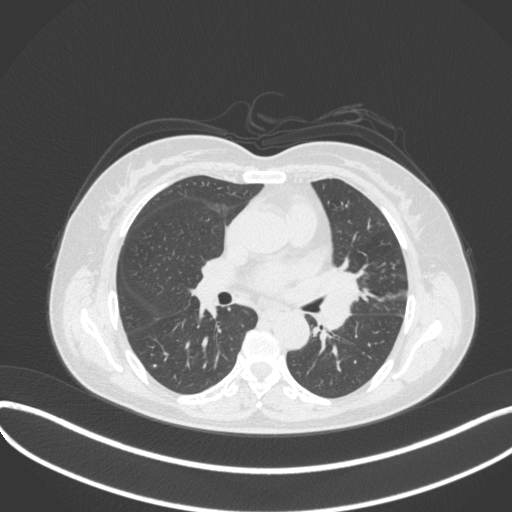
Chest CT, one axial slice; slice 191 of 373 in the series (ordered by position); reconstruction kernel B31f; 120 kVp; lung window (W 1500 / L -600 HU); 1 mm slice thickness; 512 × 512 image matrix, field of view 400 × 400 mm. Patient: female, 54 years. From the clinical record (not read from this slice): clinical TNM (as recorded): T2a N1 M0; histopathological grade: G3.
Annotated regions visible in this slice (bounding box drawn by a radiologist):
- lung tumour (recorded histology: small cell carcinoma): box from (x=317, y=268) to (x=363, y=335) px